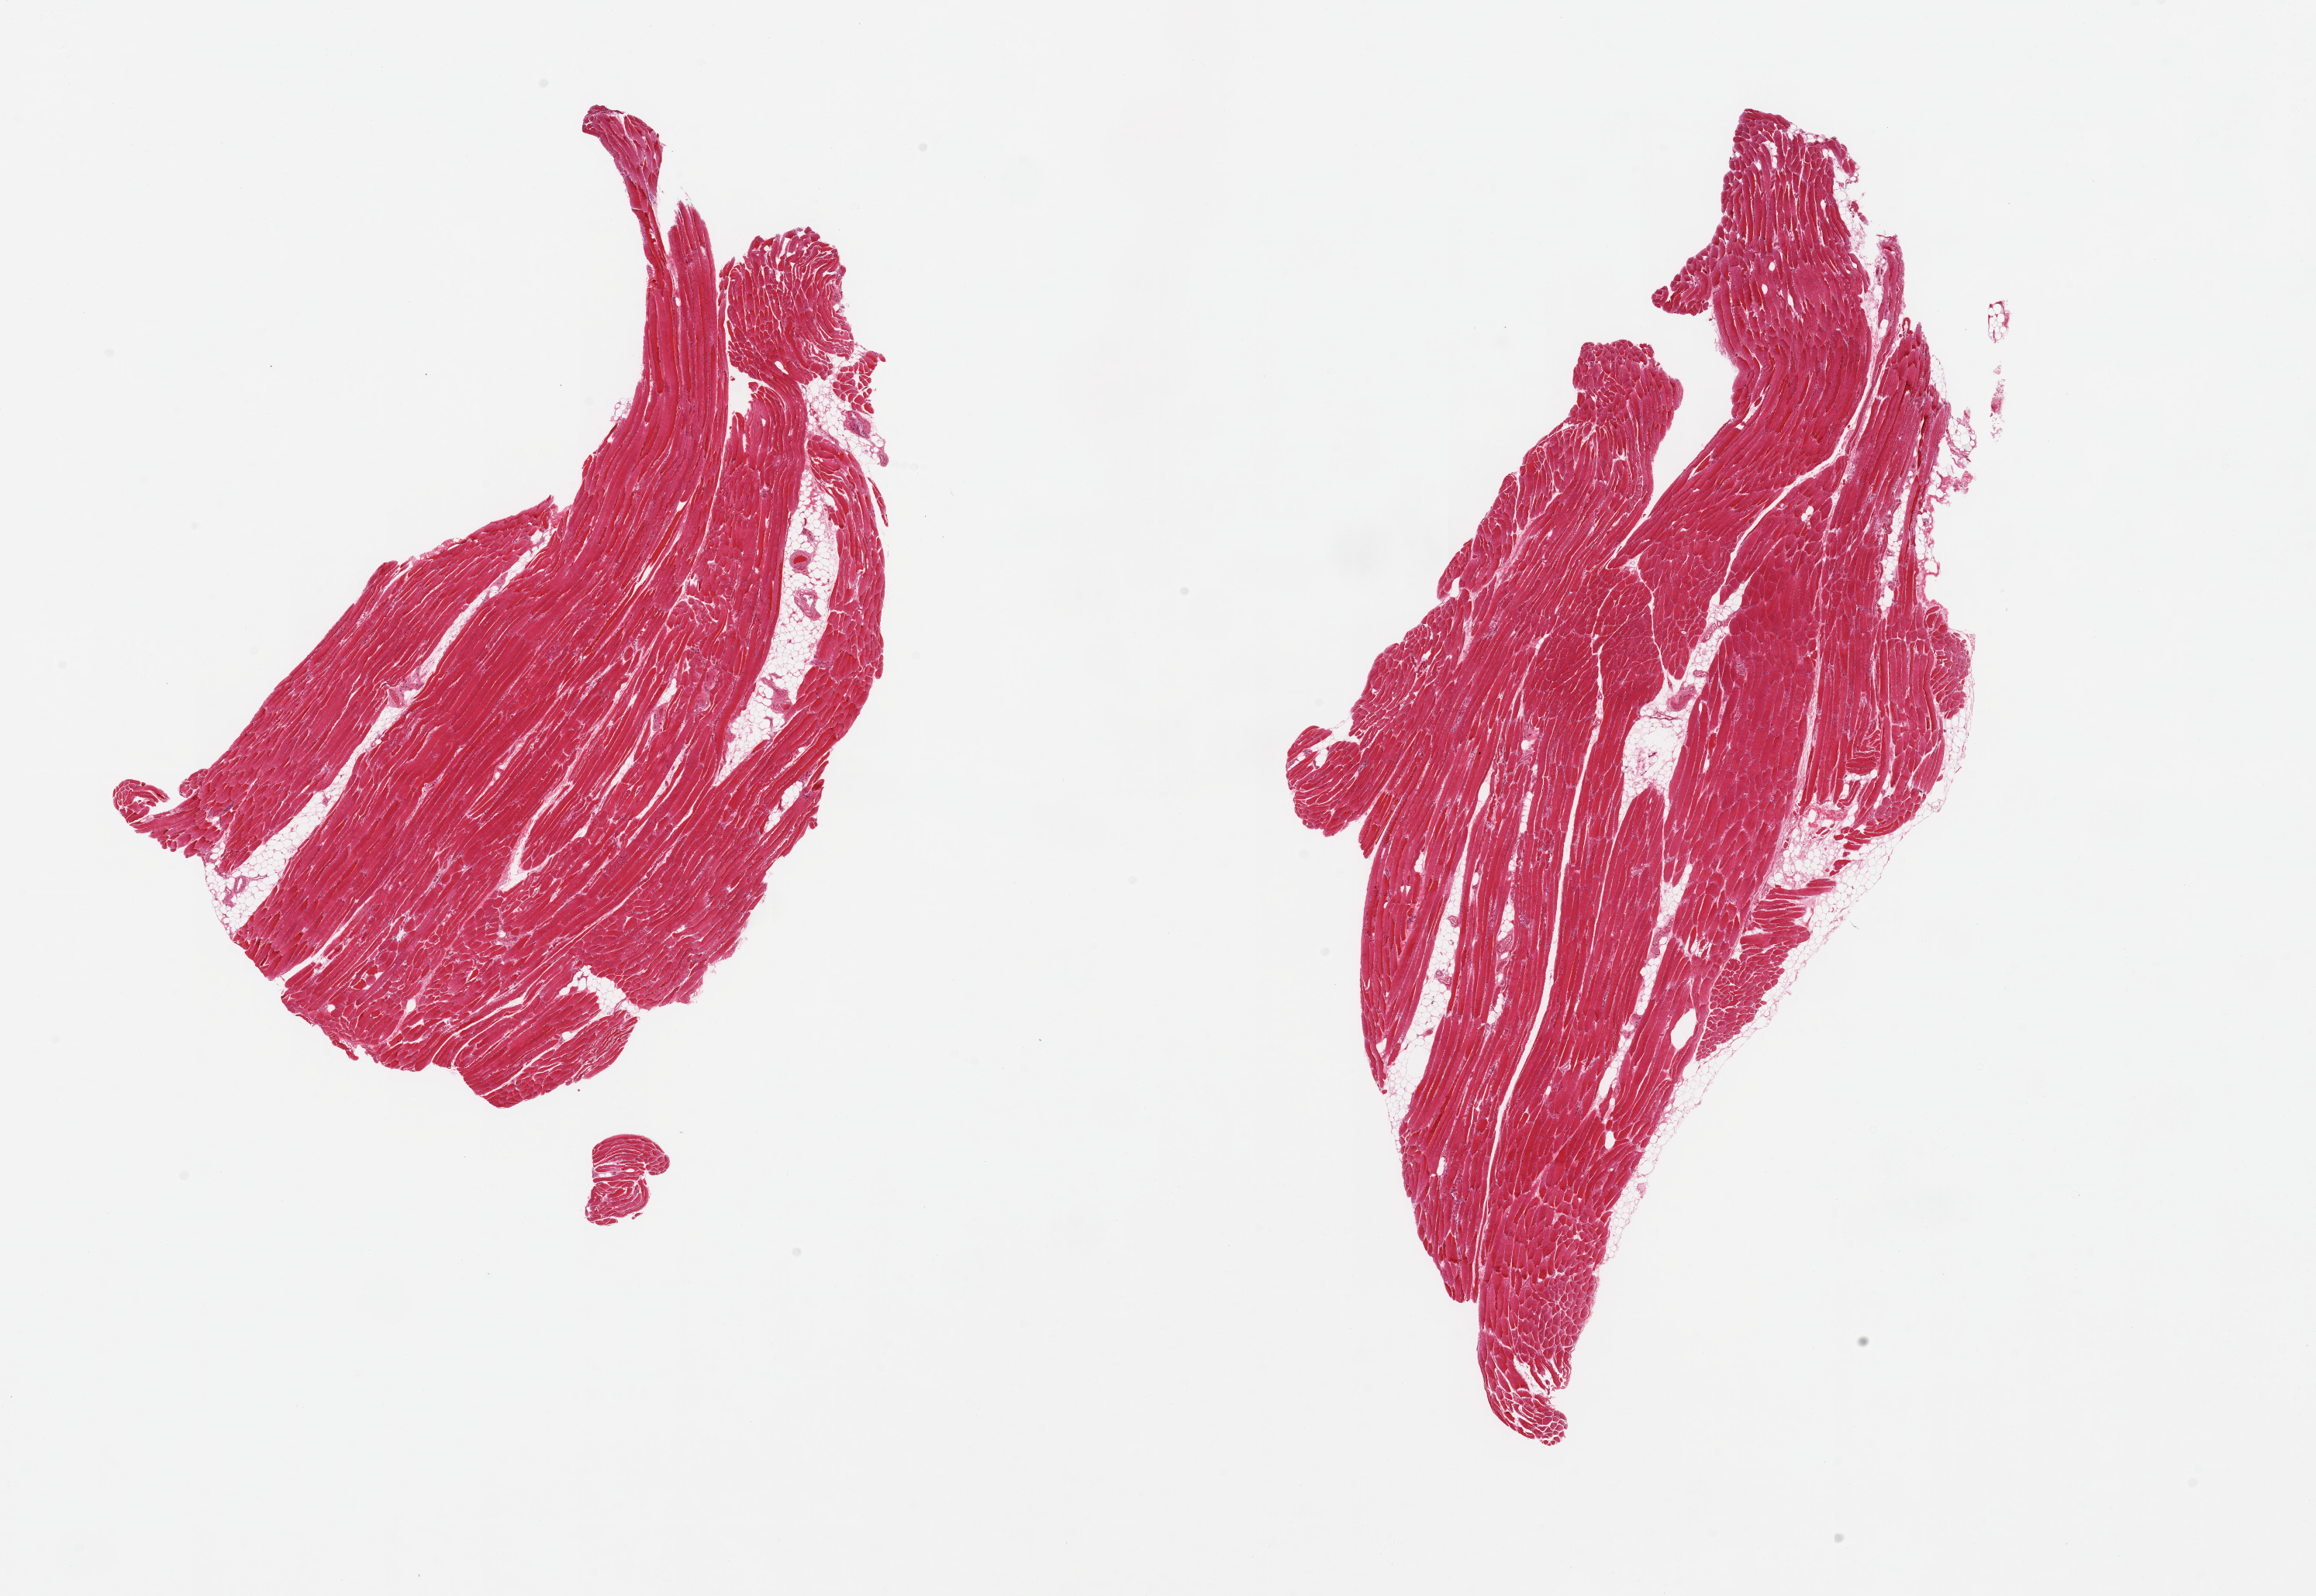
Digitized haematoxylin and eosin-stained section, brightfield — a low-resolution overview of the entire scanned area, about 23.6 x 16.3 mm (acquisition: 20x scan). PAXgene-fixed paraffin-embedded (PFPE) section. Sampled site (target tissue): skeletal muscle. Tissue donor sample.
* reviewer comment on this tissue sample: 2 pieces, ~10% interstitial fat/vascular elements; Mild chronic myositis